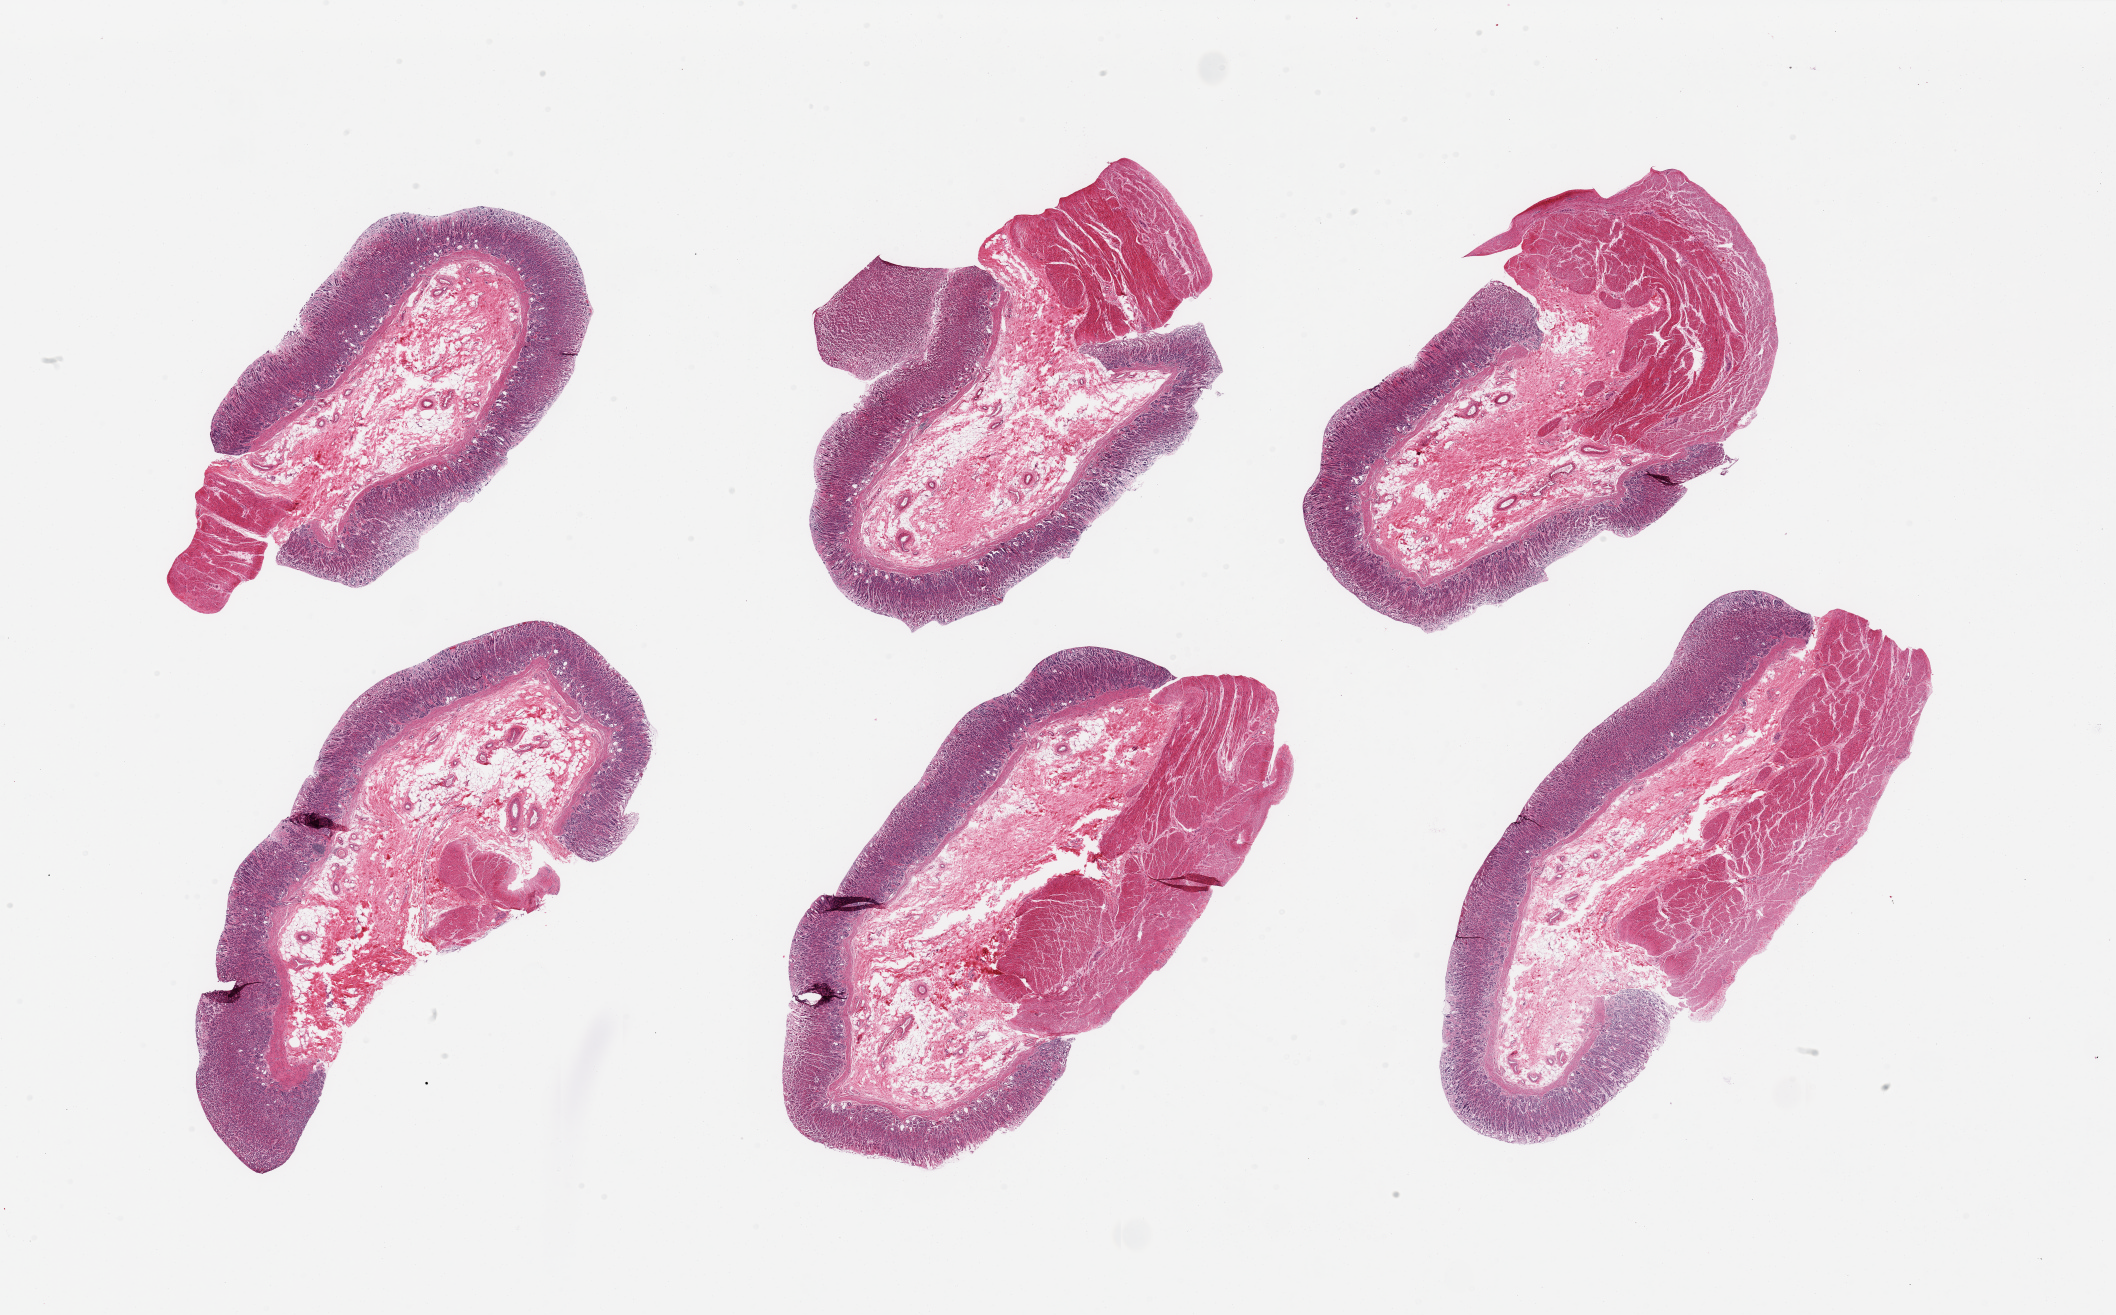
Digitized hematoxylin and eosin (H&E)-stained section, a low-resolution overview of the entire scanned area, about 33.5 x 20.8 mm, PAXgene-fixed paraffin-embedded (PFPE) section, section of gastroesophageal junction (target tissue), donor tissue sample. Donor sex: female.
Pathologist's review note for this sample: 6 pieces; gastric mucosa and muscularis.